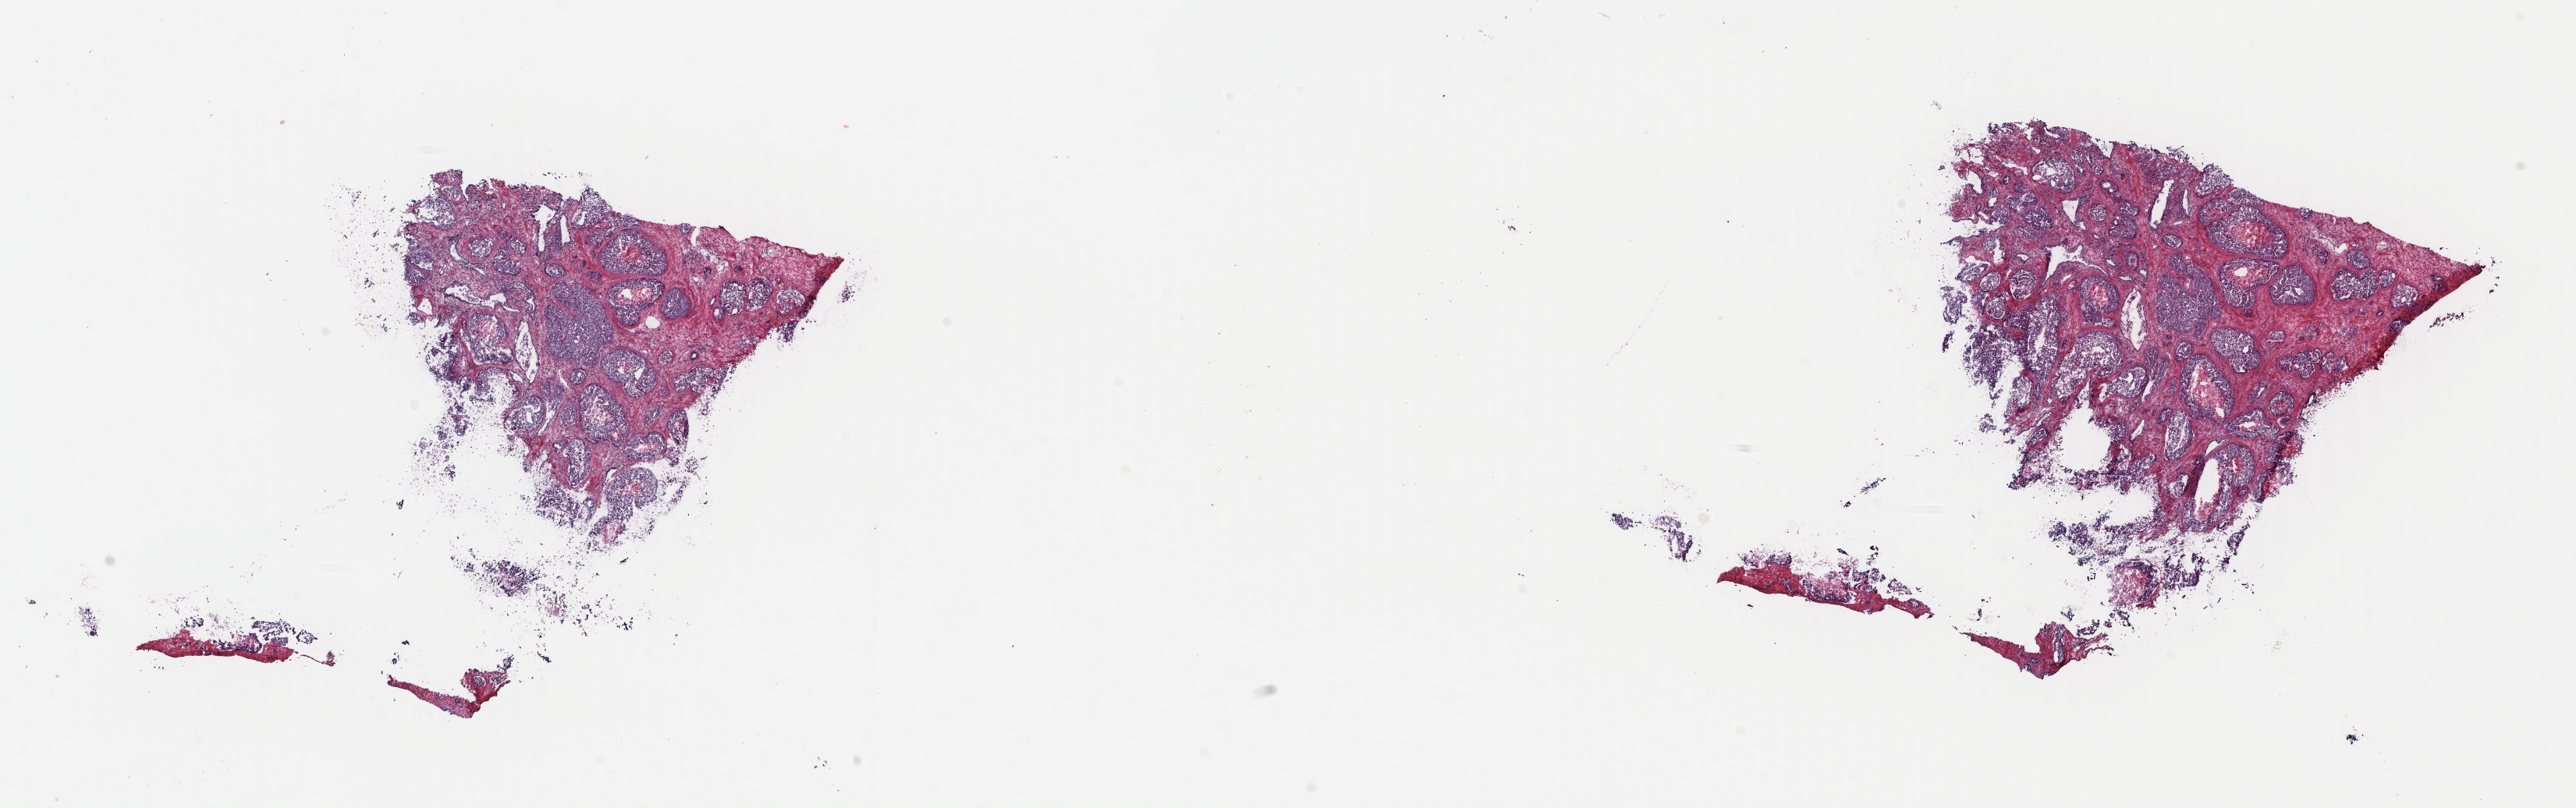
H&E-stained whole-slide image, whole scanned area (about 26.0 x 8.1 mm, from a 40x scan) shown as a low-resolution overview. Frozen section from the top of the tissue portion. Sample: primary tumour, prostate. Patient: male, age at initial diagnosis 57 years. Gleason score: 9 (4+5). Composition of this section per pathologist review: tumour cells 75%, tumour nuclei 70%, normal cells 0%, stromal cells 15%, necrosis 10%. Inflammatory infiltration, as recorded: lymphocyte infiltration 0%, monocyte infiltration 0%, neutrophil infiltration 0%.
Lymph nodes positive (case pathology): 5 of 24 examined. Pathologic diagnosis: Adenocarcinoma, NOS (prostate gland).